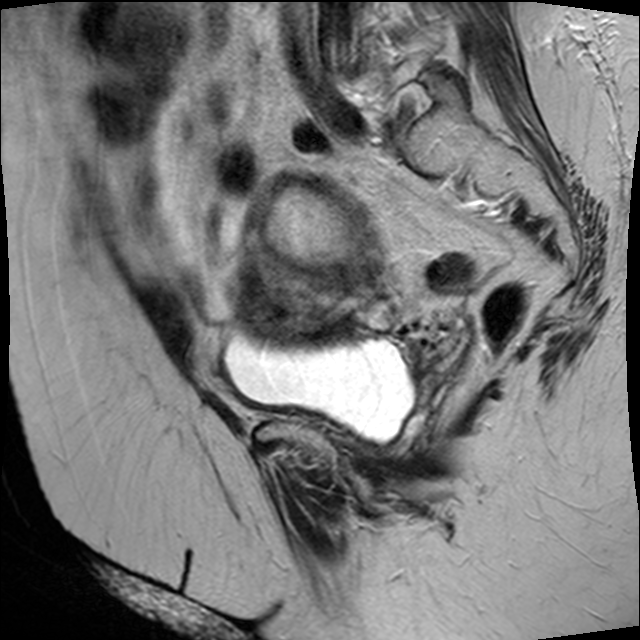
Pelvic MRI for cervical cancer, one sagittal slice. Slice 28 of 45 in the series (ordered by position). T2-weighted. 1.5 T. TE 89 ms, TR 4610 ms. 4 mm slice thickness. 640 × 640 image matrix, field of view 260 × 260 mm. Patient: female, 50 years.
Annotated regions visible in this slice (expert manual segmentation):
- uterus and cervix: bounding box [x1, y1, x2, y2] px = [212, 169, 487, 404]